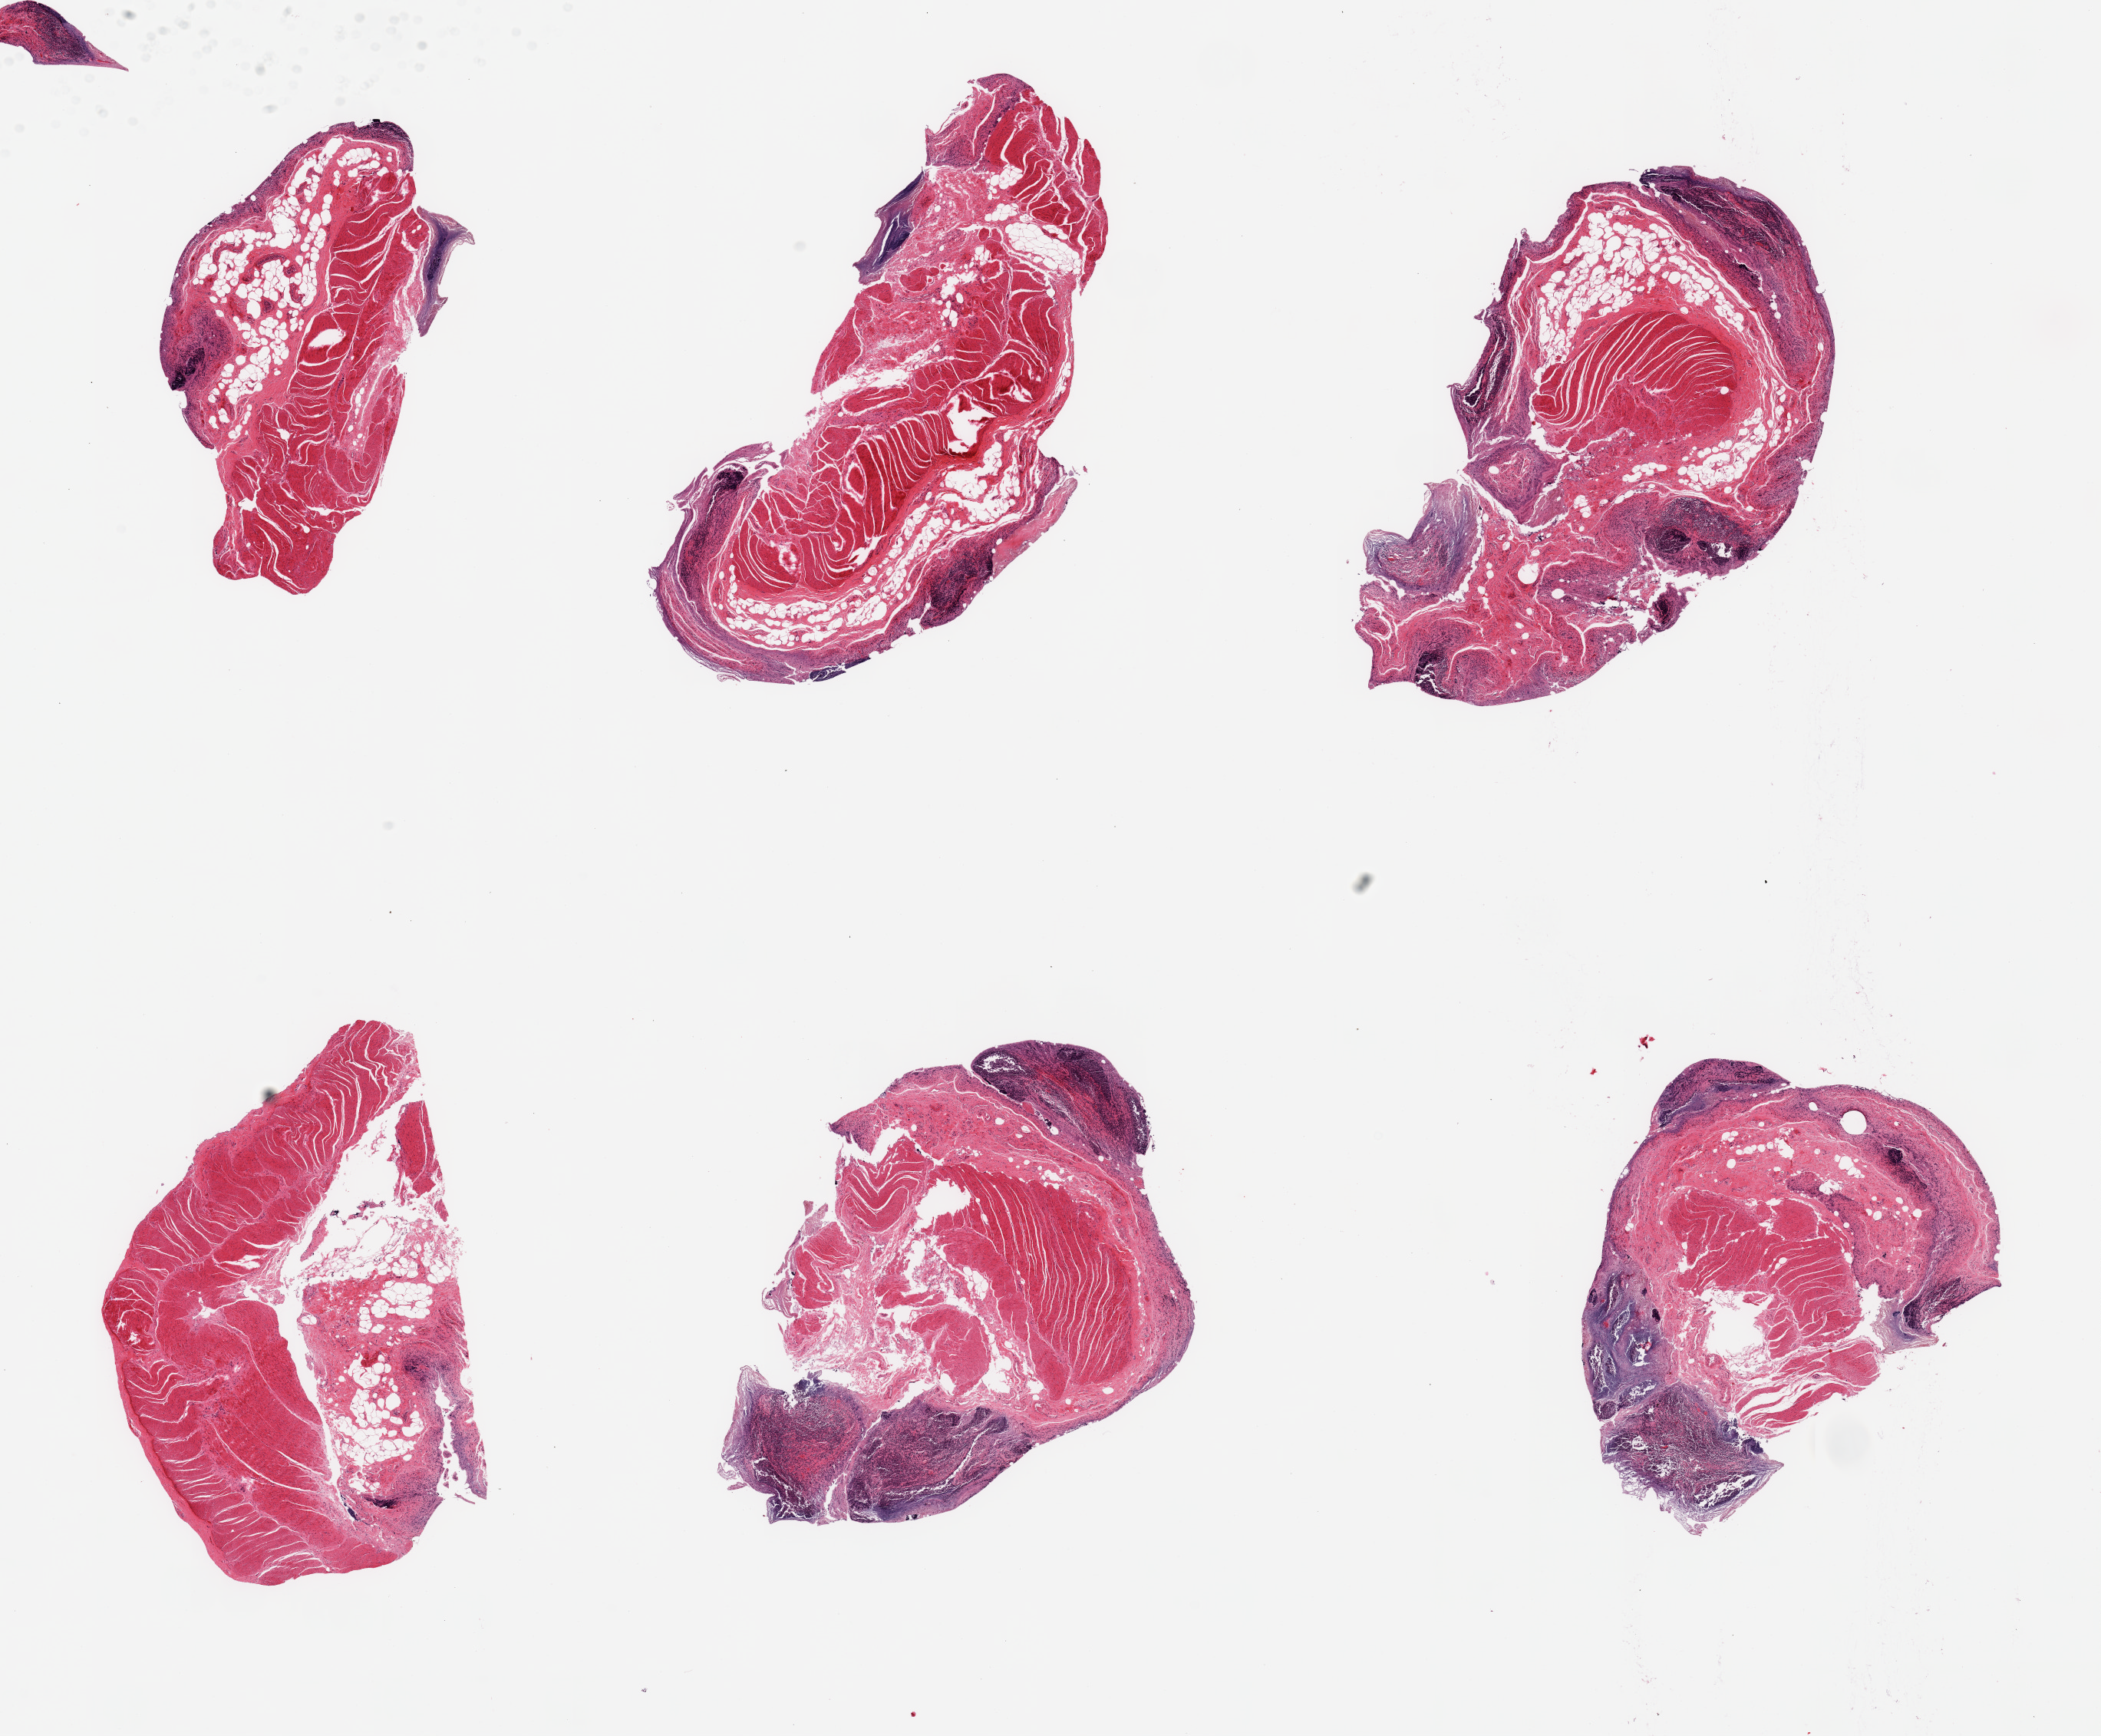
Hematoxylin and eosin (H&E) whole-slide image — low-resolution overview of the scanned area, about 21.7 x 17.9 mm. PAXgene-fixed paraffin-embedded (PFPE) section. Section of ileum (target tissue). Tissue donor sample. Donor sex: male.
• reviewer comment on this tissue sample: 6 pieces; muscularis and autolyzed mucosa with some residual target lymphoid aggregates